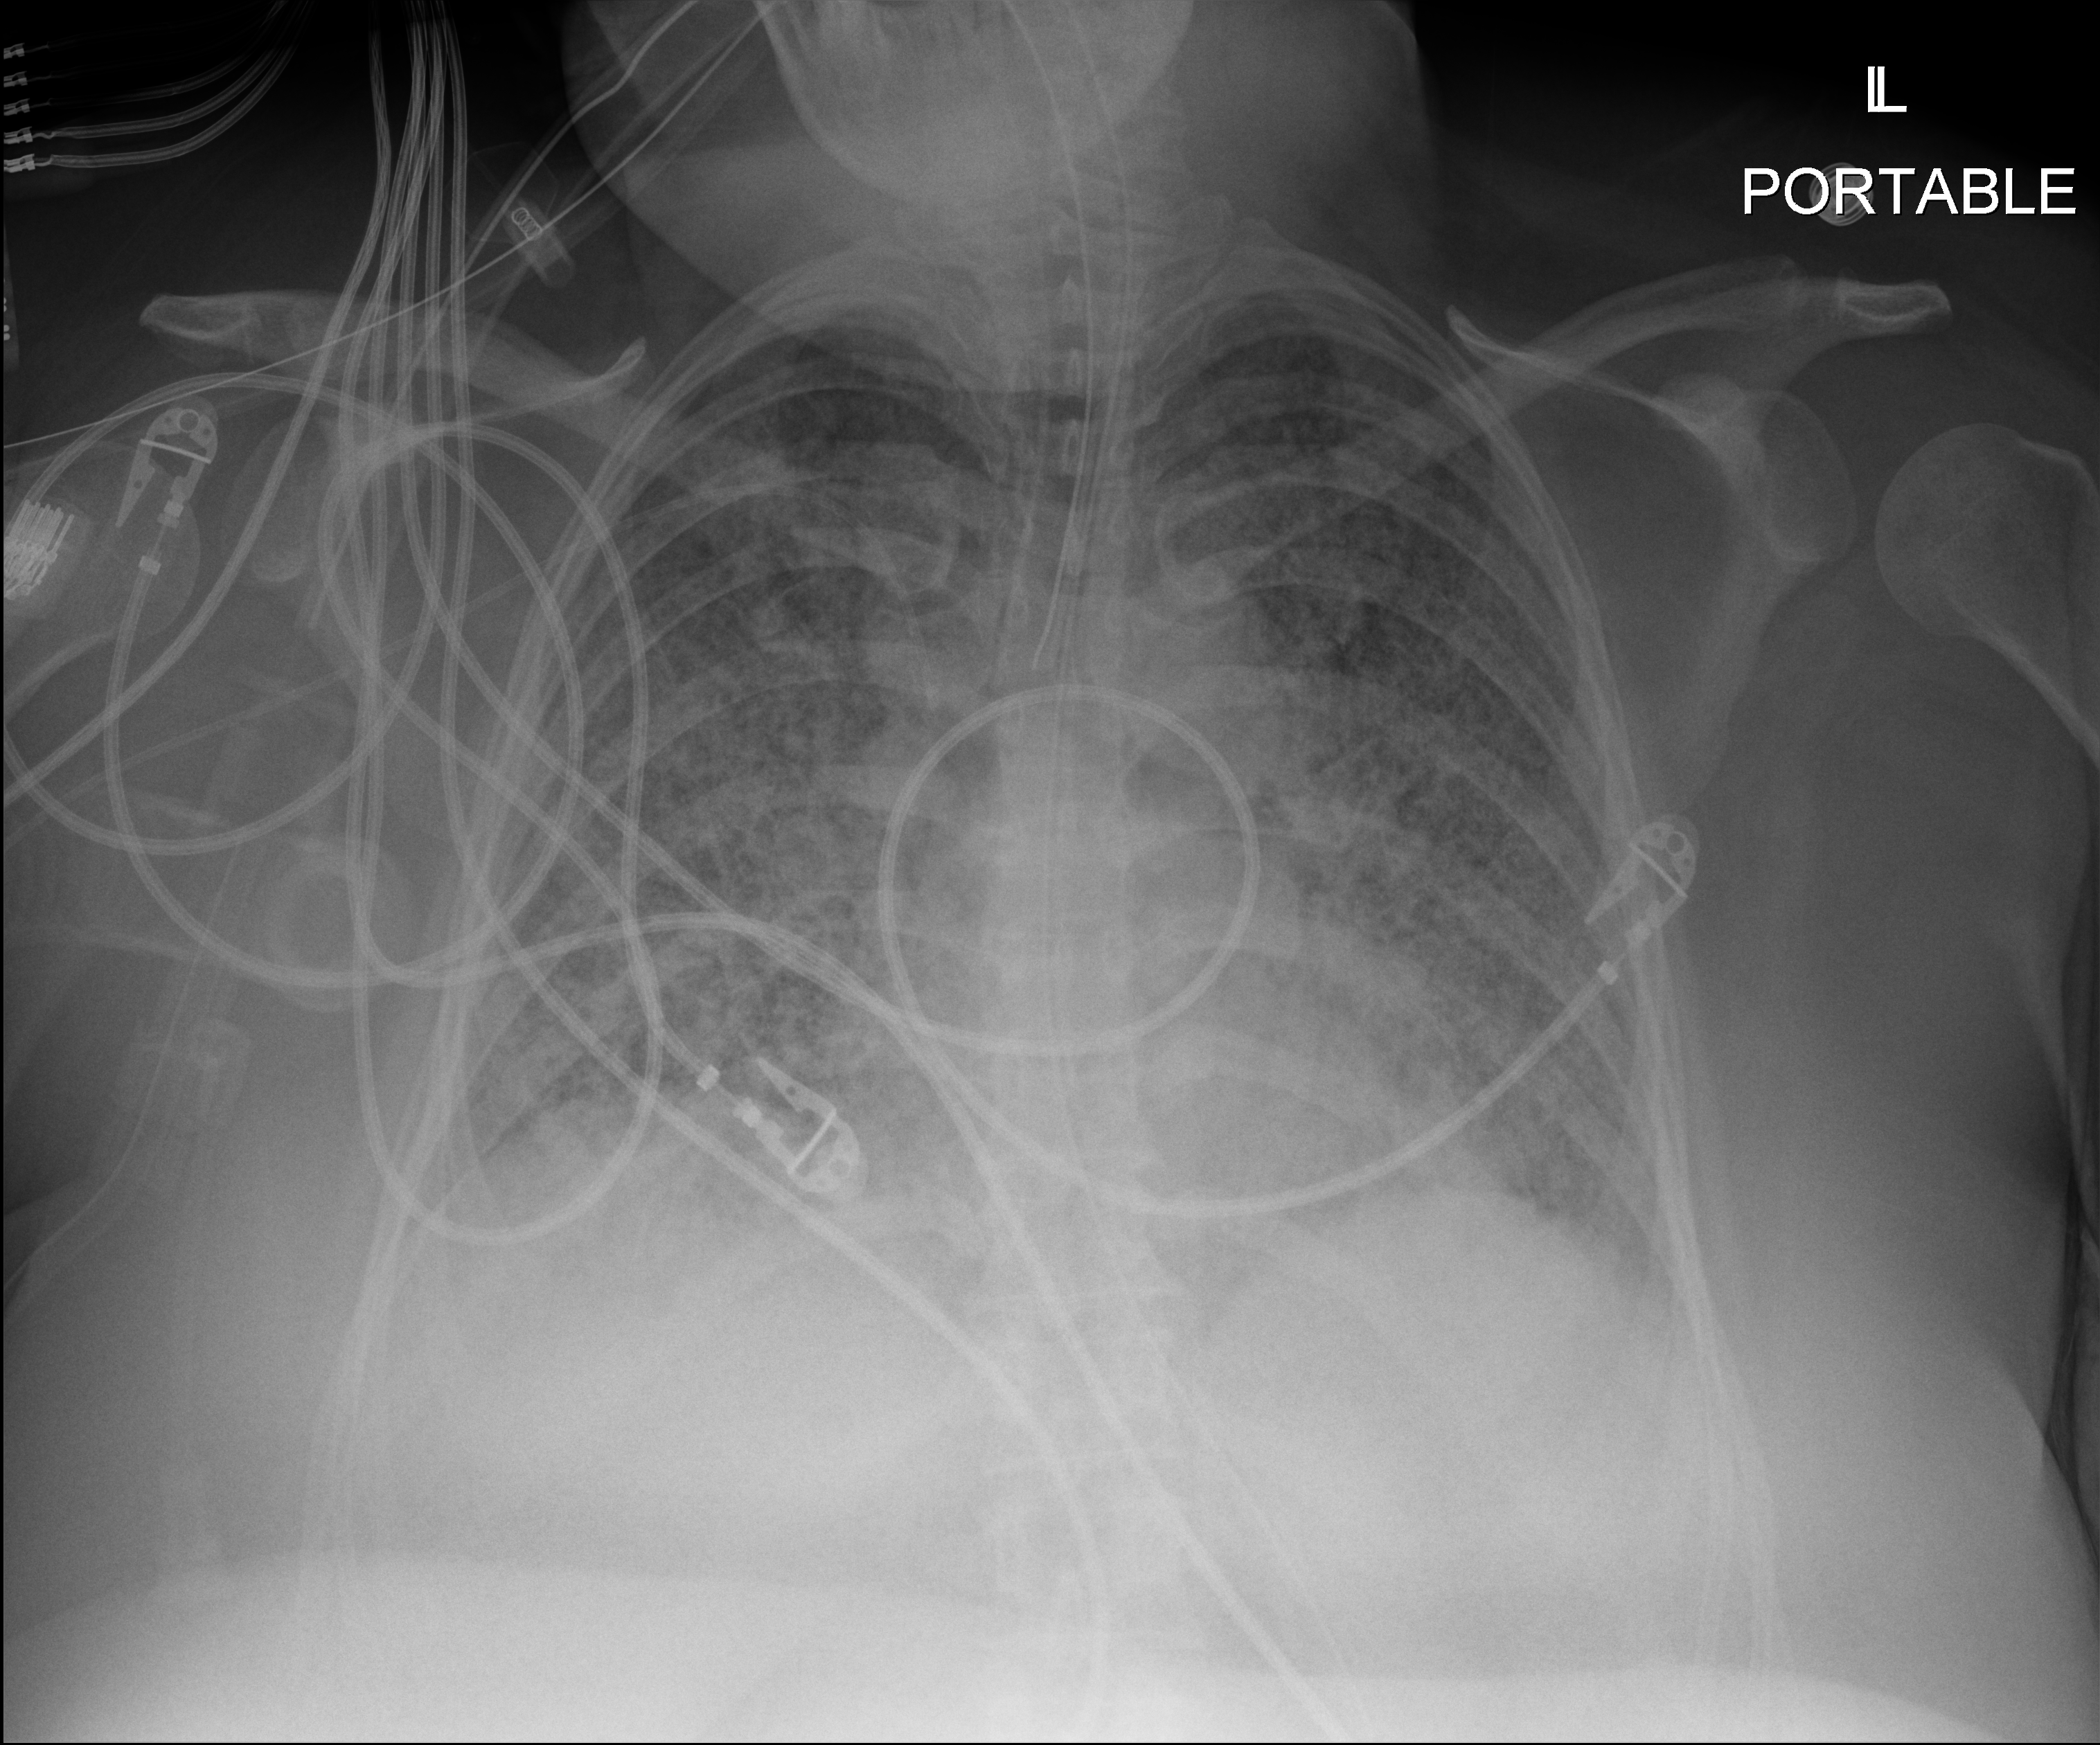
Portable chest radiograph, anteroposterior (AP) projection. Patient hospitalised with COVID-19; female, aged 18–59 years.
From the hospital-stay record, not from the radiograph (when in the stay this image was taken is not recorded): COPD (admission record): no; admitted to intensive care during this hospital stay: yes.